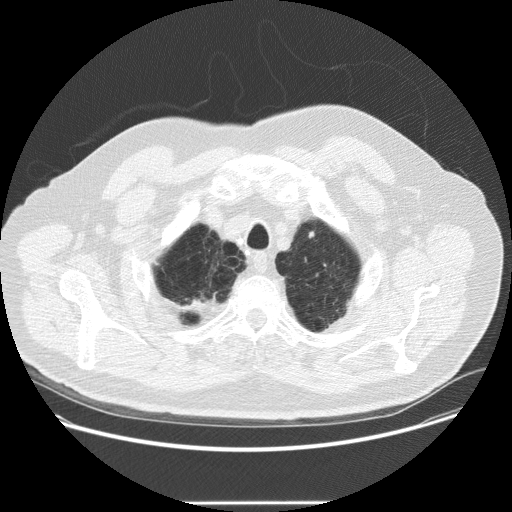
Chest CT (low-dose screening protocol), one axial image; second annual screen; lung window (W 1500 / L -600 HU); slice 44 of 265 in the series; 512 × 512 image matrix. Male participant, aged 64 years at enrolment. Current smoker at enrolment.
Expert reader's lesion annotation, bounding box (x1, y1, x2, y2) in pixels: (298, 224, 326, 250). Reader record for this screening exam (exam-level; its link to the box is not recorded): non-calcified nodule or mass ≥4 mm, left upper lobe, 5 × 3 mm, smooth margins, soft tissue attenuation, pre-existing on the prior screen: no. Participant outcome: lung cancer diagnosed 300 days after this screen — adenocarcinoma, NOS, left upper lobe, poorly differentiated (G3), stage IA (AJCC 6th edition), 8 mm at pathology.